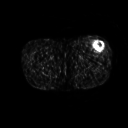
FDG PET of an extremity soft-tissue mass (from a PET/CT study), one axial slice. Slice 224 of 267 in the series (ordered by position). 3.27 mm slice thickness. 128 × 128 image matrix. Male patient, age 64 years. From the clinical record (not read from this slice): histological type: extraskeletal osteosarcoma; grade: high; site of the primary tumour: thigh.
Structures marked on this image (expert contour drawn on MRI and transferred to this co-registered scan by the dataset authors):
- gross tumour volume (mass): bounding box [x1, y1, x2, y2] px = [92, 41, 104, 51]